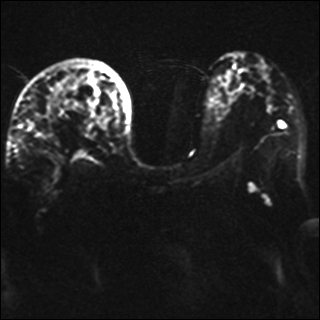
Breast MRI, one axial slice. Position 21 of 42 along the scan axis. Diffusion-weighted series; image 2 of 4 stored at this slice position (different b-values; order by instance number). 1.5 T. 4 mm slice thickness. 320 × 320 image matrix, field of view 330 × 330 mm. Female patient.
Annotated regions visible in this slice (expert manual segmentation):
- tumour on diffusion-weighted imaging: bounding box <46,99,55,117> (left, top, right, bottom; pixels)